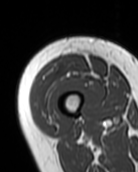
MRI of an extremity soft-tissue mass, one axial slice. Position 19 of 99 along the scan axis. MR volume resampled by the dataset authors to the PET/CT grid (not the native acquisition matrix). 138 × 172 image matrix. Female patient. Case-level facts recorded for this patient, not image findings: histological type: pleiomorphic undifferentiated sarcoma; grade: high; site of the primary tumour: right quadricep.
Annotated regions visible in this slice (expert contour drawn on MRI and transferred to this co-registered scan by the dataset authors):
- gross tumour volume including surrounding oedema: bounding box <32,55,86,117> (left, top, right, bottom; pixels)